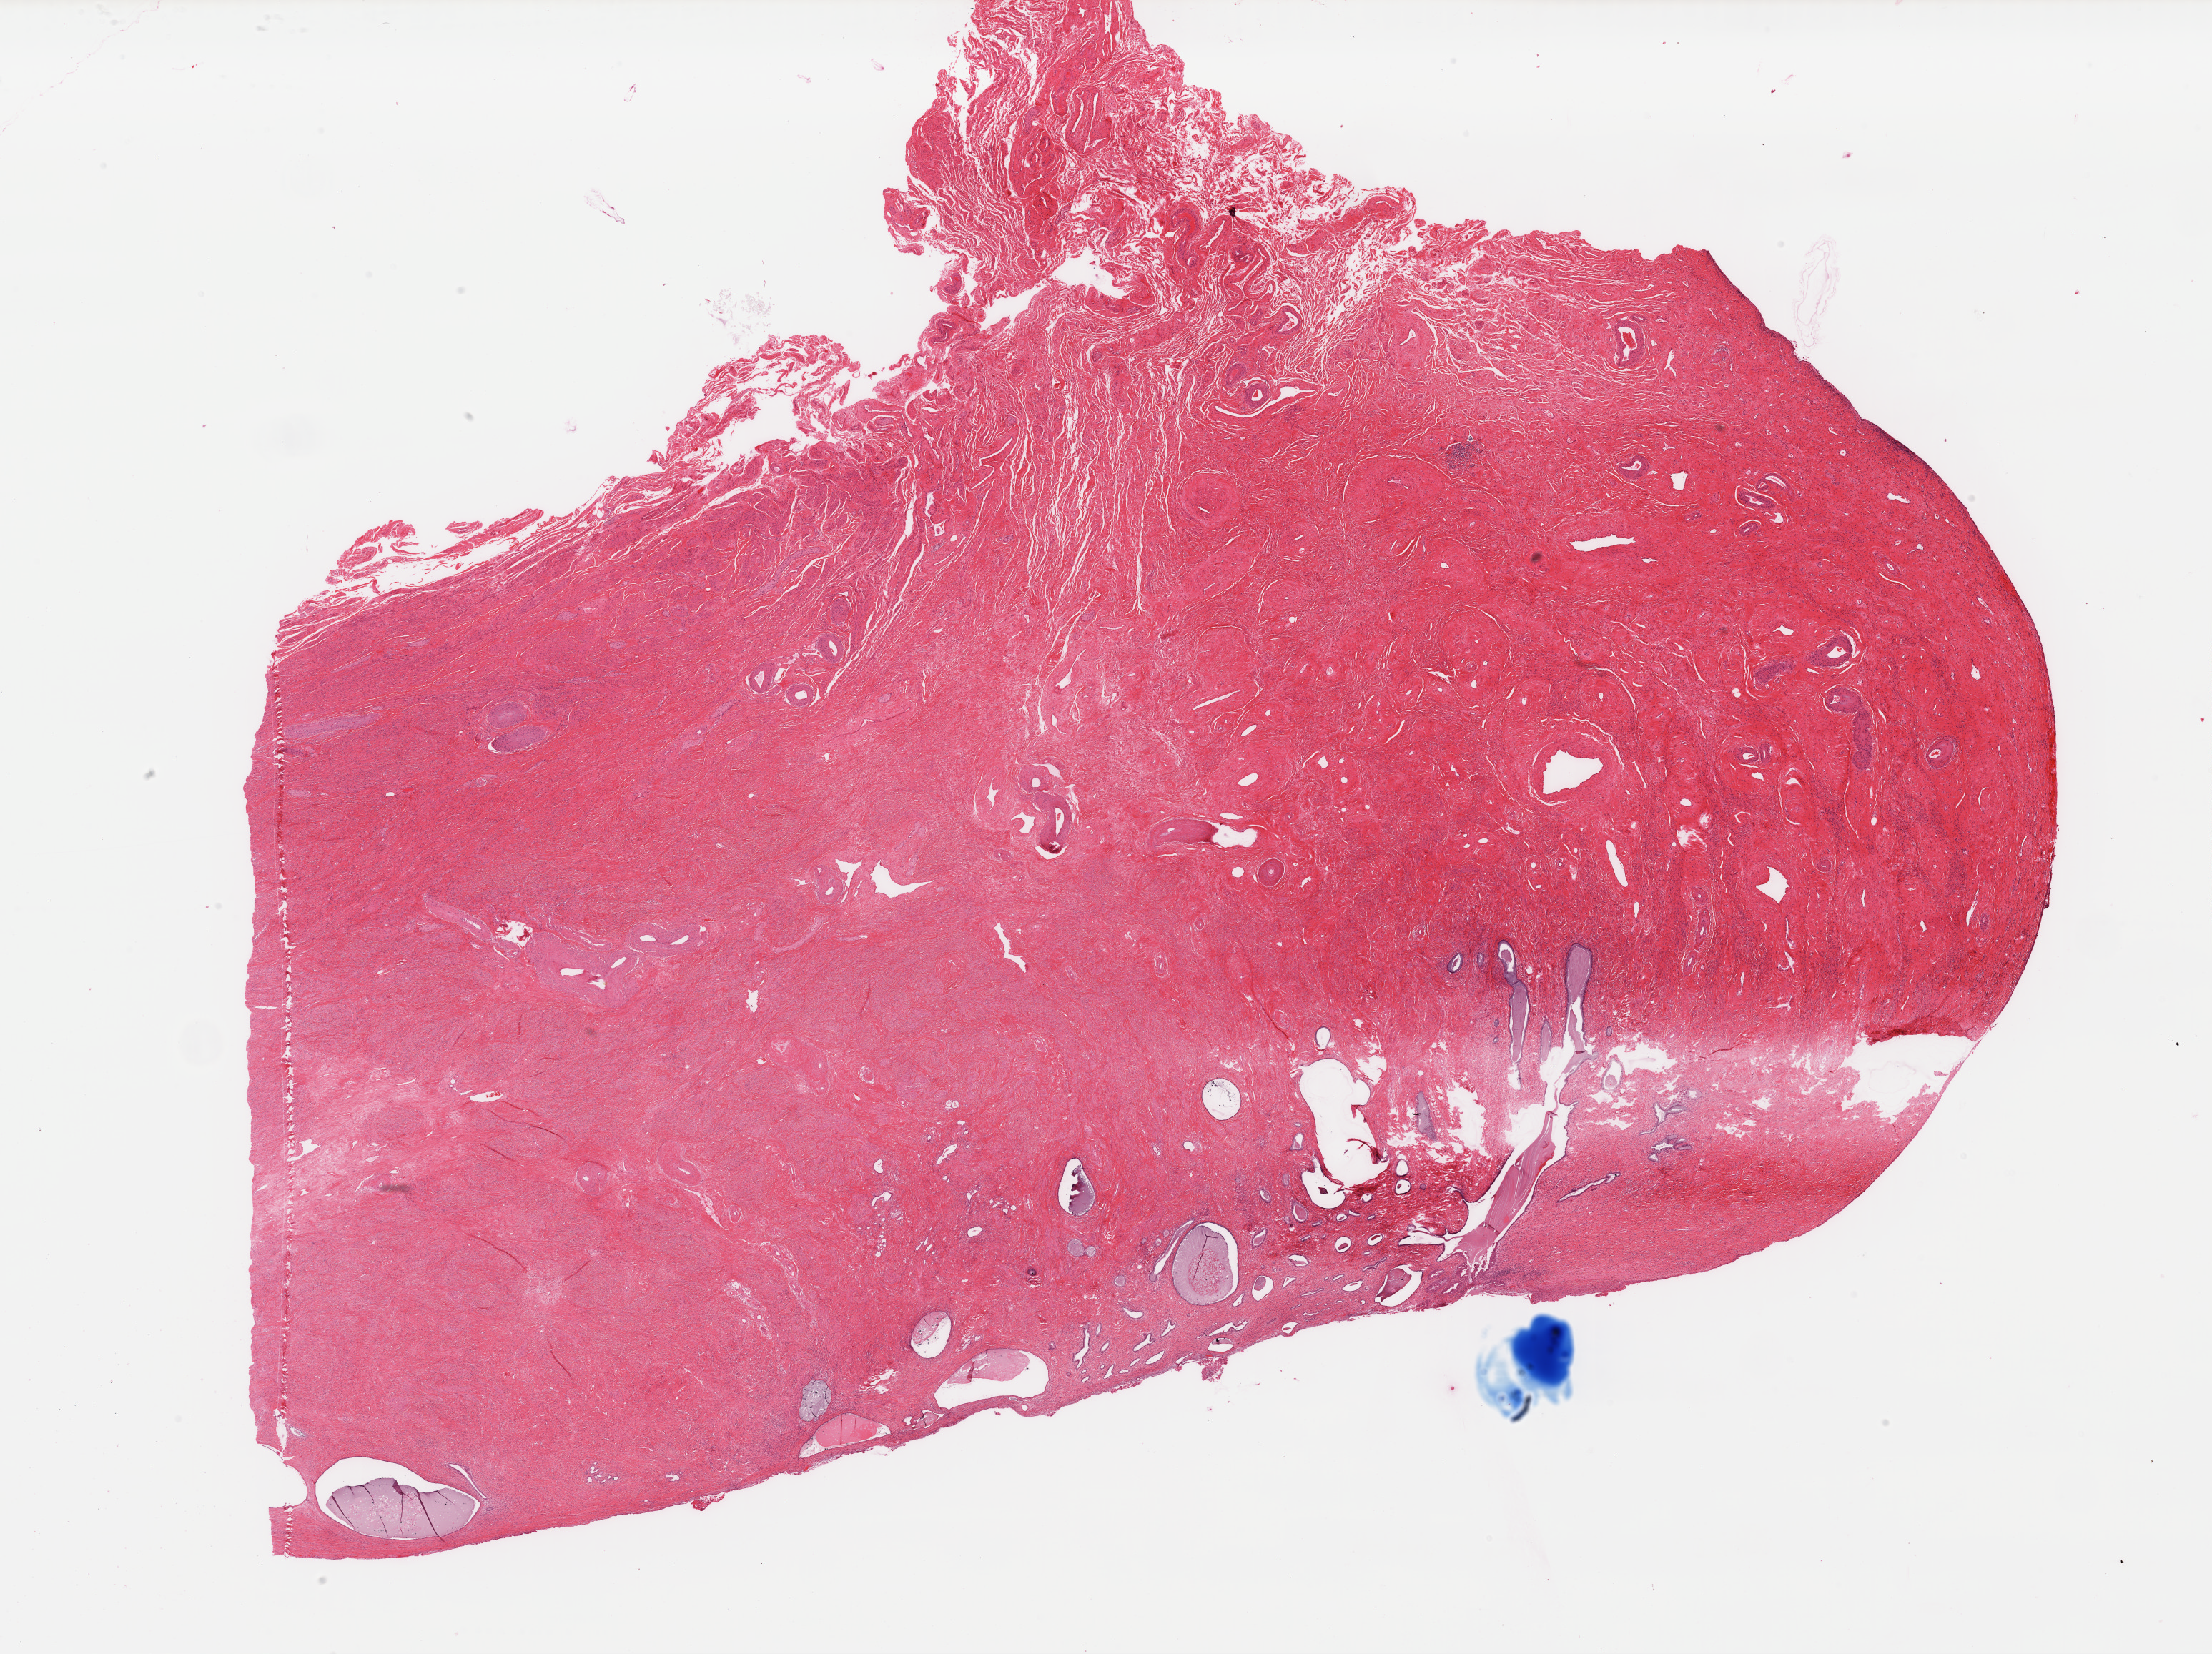
H&E whole-slide image — a low-resolution overview of the entire scanned area, about 24.4 x 18.3 mm (acquisition: 40x scan); formalin-fixed paraffin-embedded (FFPE) diagnostic section; primary tumour sample from the uterus. Patient: female, age at initial diagnosis 72 years. Histologic grade: G3 (poorly differentiated).
Diagnosis: Endometrioid adenocarcinoma, NOS (endometrium). FIGO stage: IIA. Lymph nodes positive (case pathology): 0 of 8 examined.